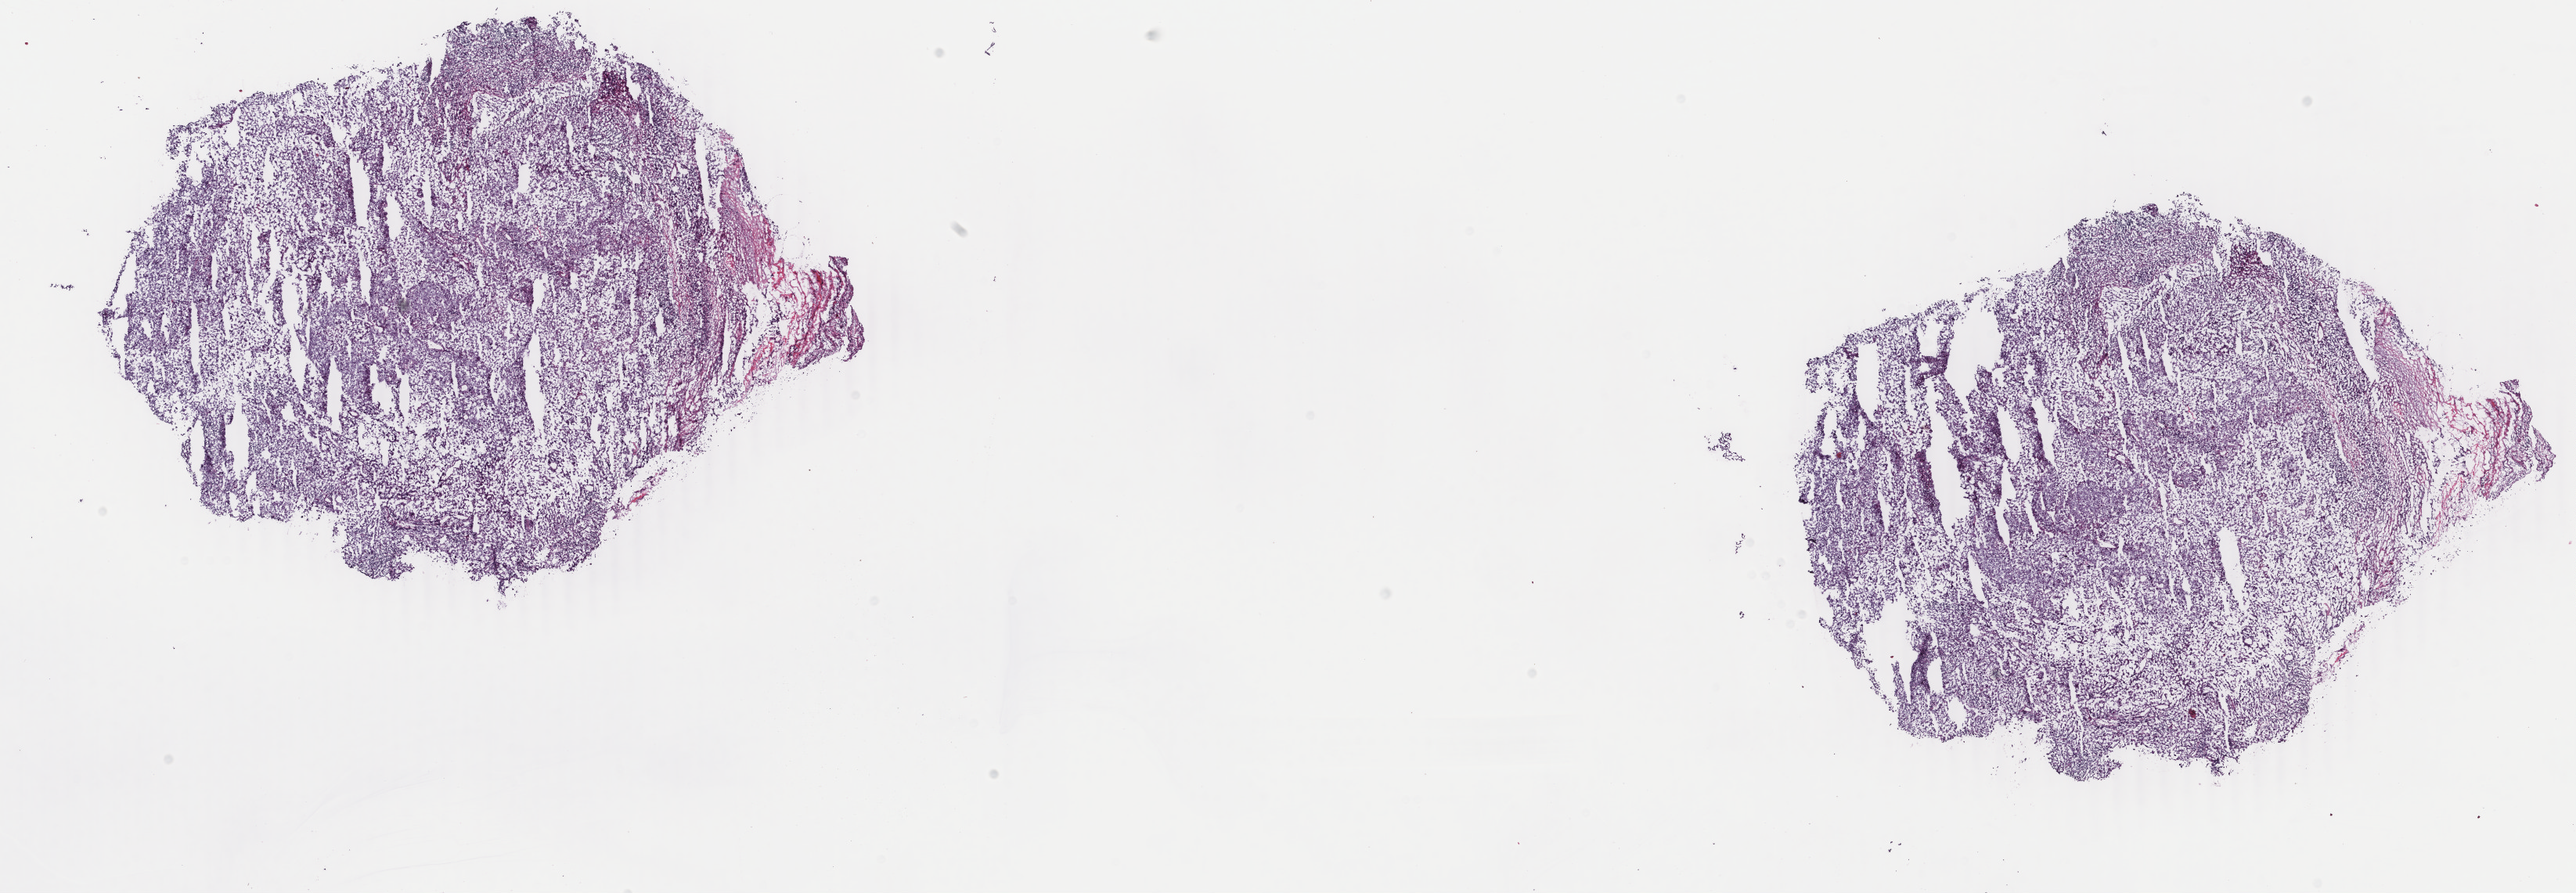
Hematoxylin and eosin (H&E) stained whole-slide image — low-resolution overview of the scanned area, about 26.2 x 9.1 mm (slide scanned at 40x); frozen section from the top of the tissue portion; metastatic tumour sample, sampled site: lymph node. Female, age 37 years at initial diagnosis. Pathologist review of this section (percent, as recorded): tumour cells 85%, tumour nuclei 85%, normal cells 0%, stromal cells 15%, necrosis 0%. Infiltration values recorded for this section: lymphocyte infiltration 5%, monocyte infiltration 0%, neutrophil infiltration 0%.
This section: metastatic tumour tissue. Patient diagnosis: Malignant melanoma, NOS.